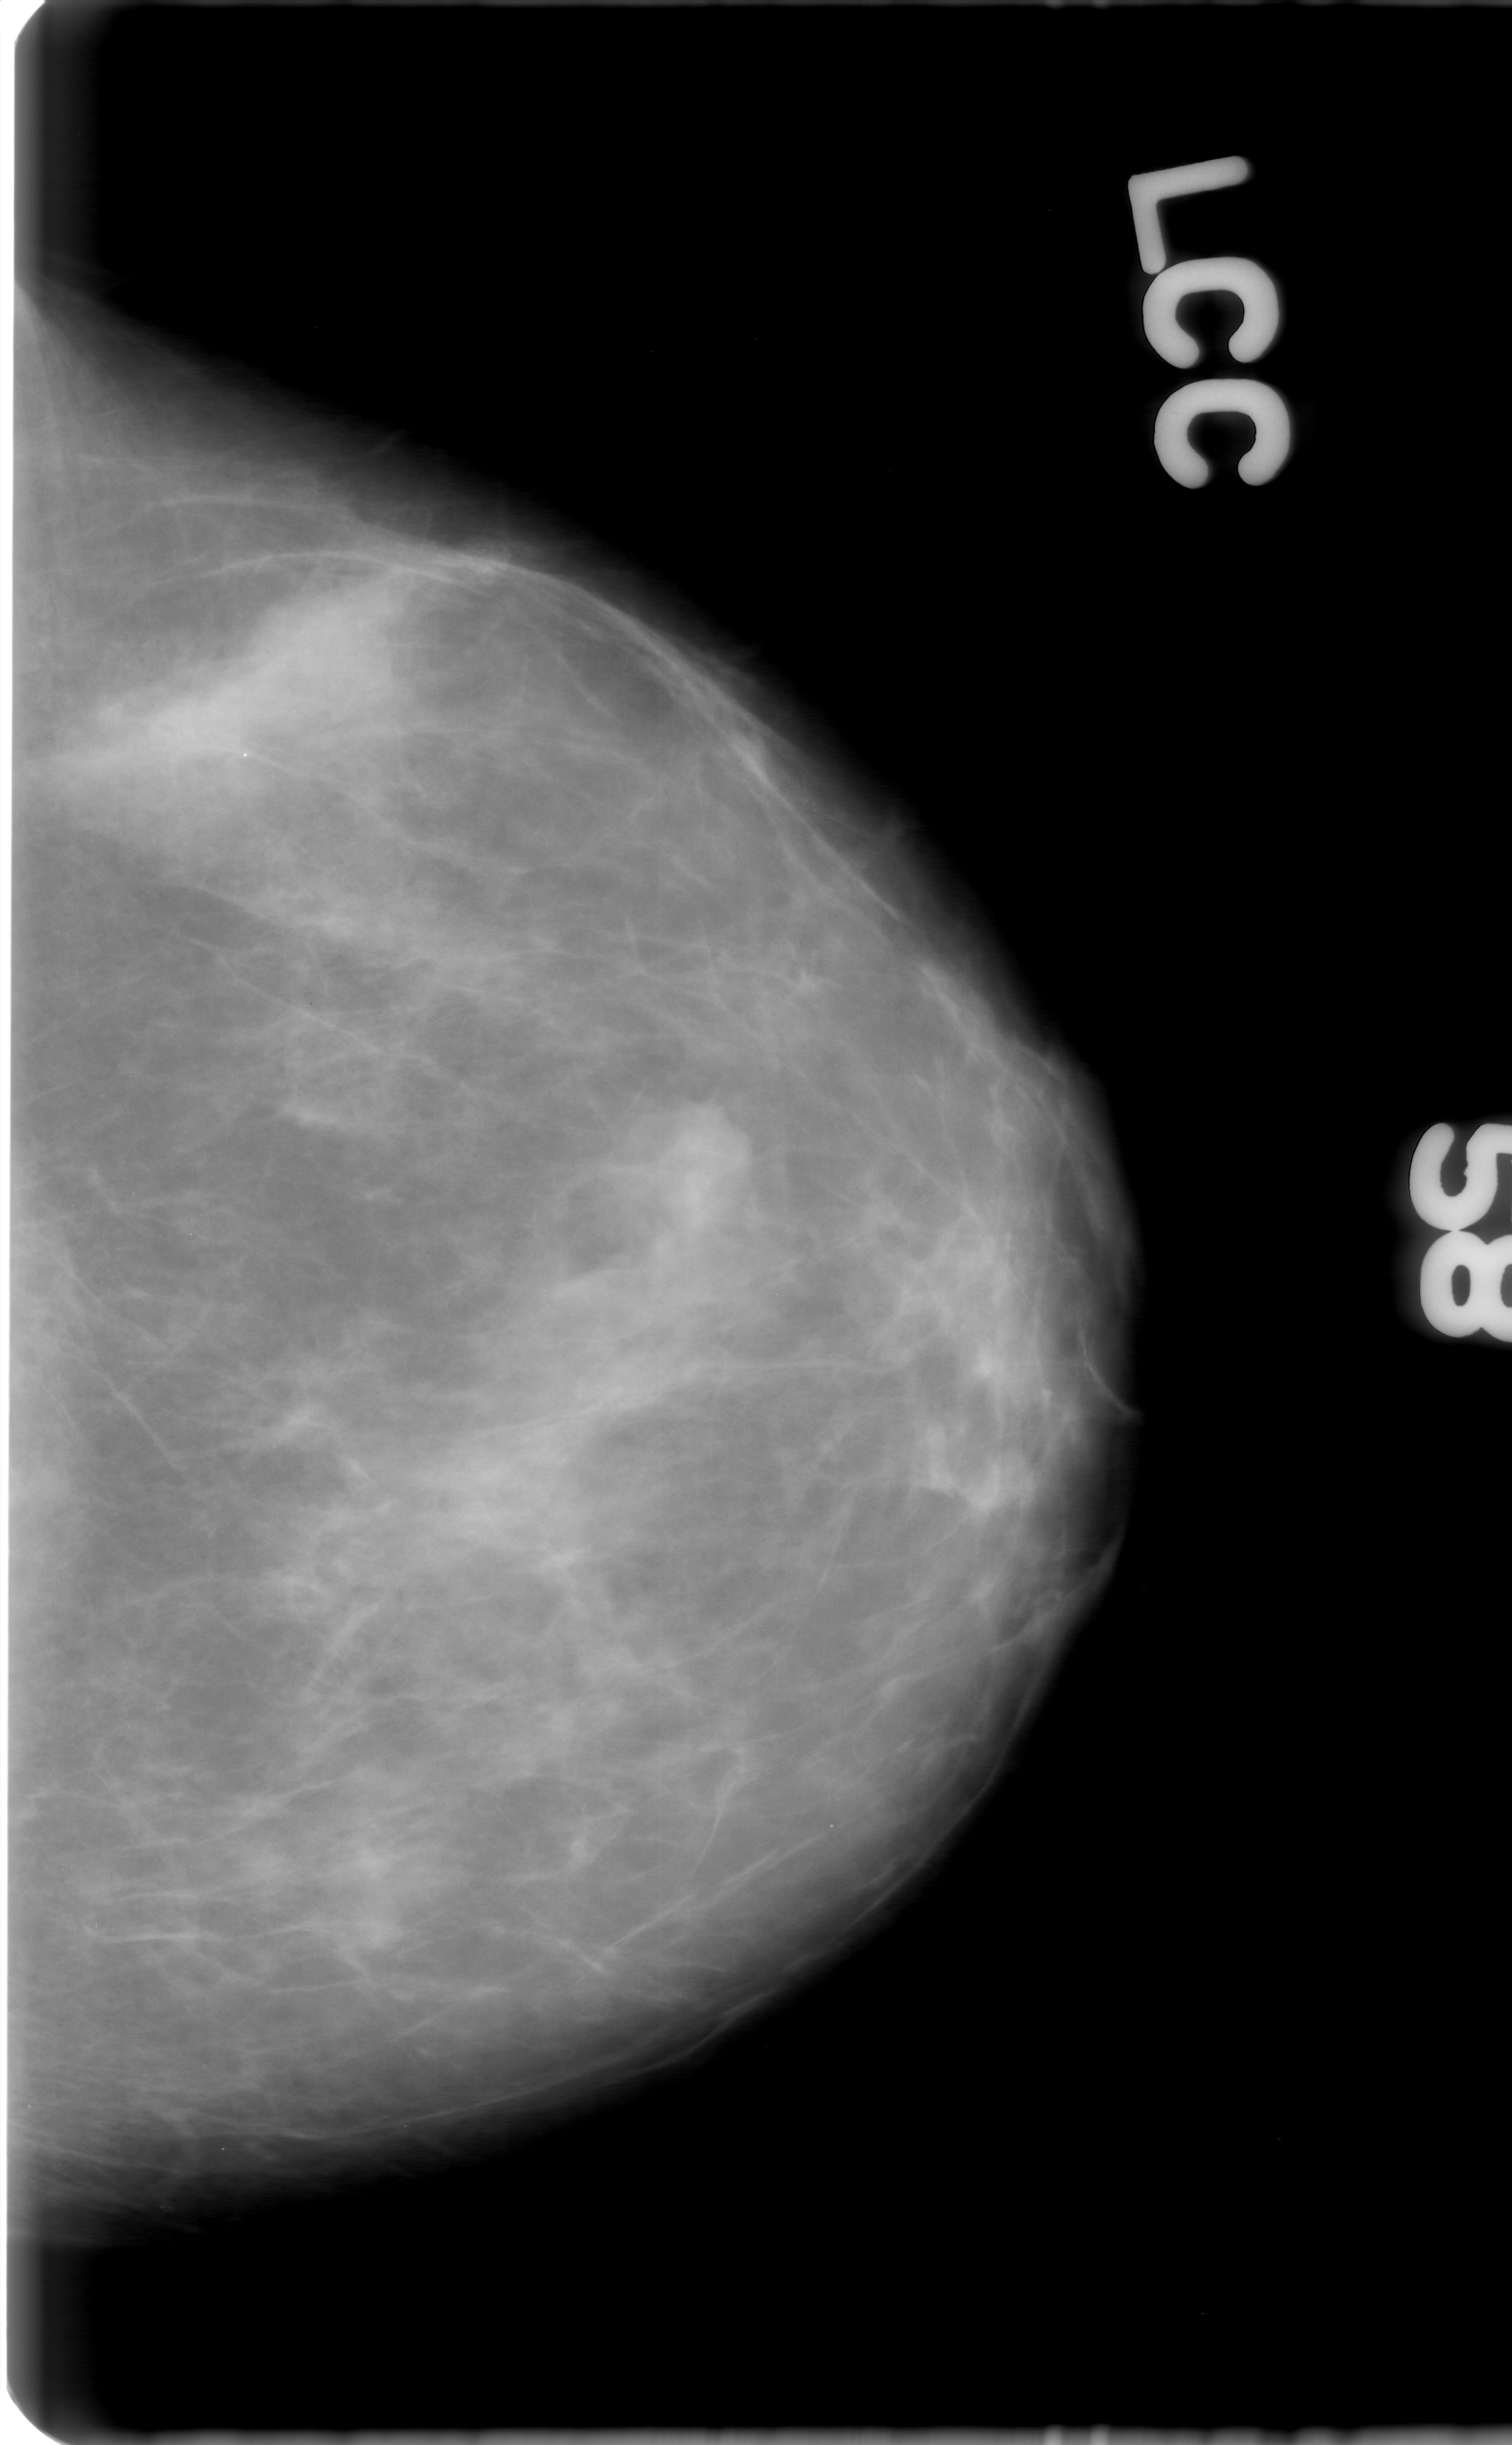
Digitized screen-film mammogram; left breast; CC view; breast composition: scattered fibroglandular densities (BI-RADS density category 2 of 4).
Marked abnormality: mass, shape oval, margins obscured; BI-RADS assessment category 0 (incomplete: needs additional imaging); pathology result (as recorded, not read from the image): benign.